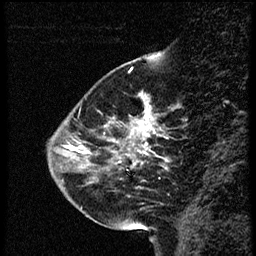
Breast MRI (dynamic contrast-enhanced), one sagittal slice; slice 14 of 56 in the series (ordered by position); dynamic contrast-enhanced study with each time point stored as its own series, time point 2 of 4 at this slice position (early post-contrast, ordered by acquisition time); 1.5 T; TE 4.2 ms, TR 18.9 ms; 2 mm slice thickness; 256 × 256 image matrix, field of view 200 × 200 mm. Female patient. Case-level facts recorded for this patient, not image findings: setting: breast cancer imaged before/during neoadjuvant chemotherapy; receptor status: HER2-positive.
Annotated regions visible in this slice (semi-automatically segmented with operator editing):
- analysis volume of interest (the breast-tissue region the enhancement analysis was run in; not a lesion): bounding box <63,80,169,215> (left, top, right, bottom; pixels)
- tumour enhancement mask (voxels above the 100 % enhancement threshold inside the analysis volume of interest): <105,94,155,163>